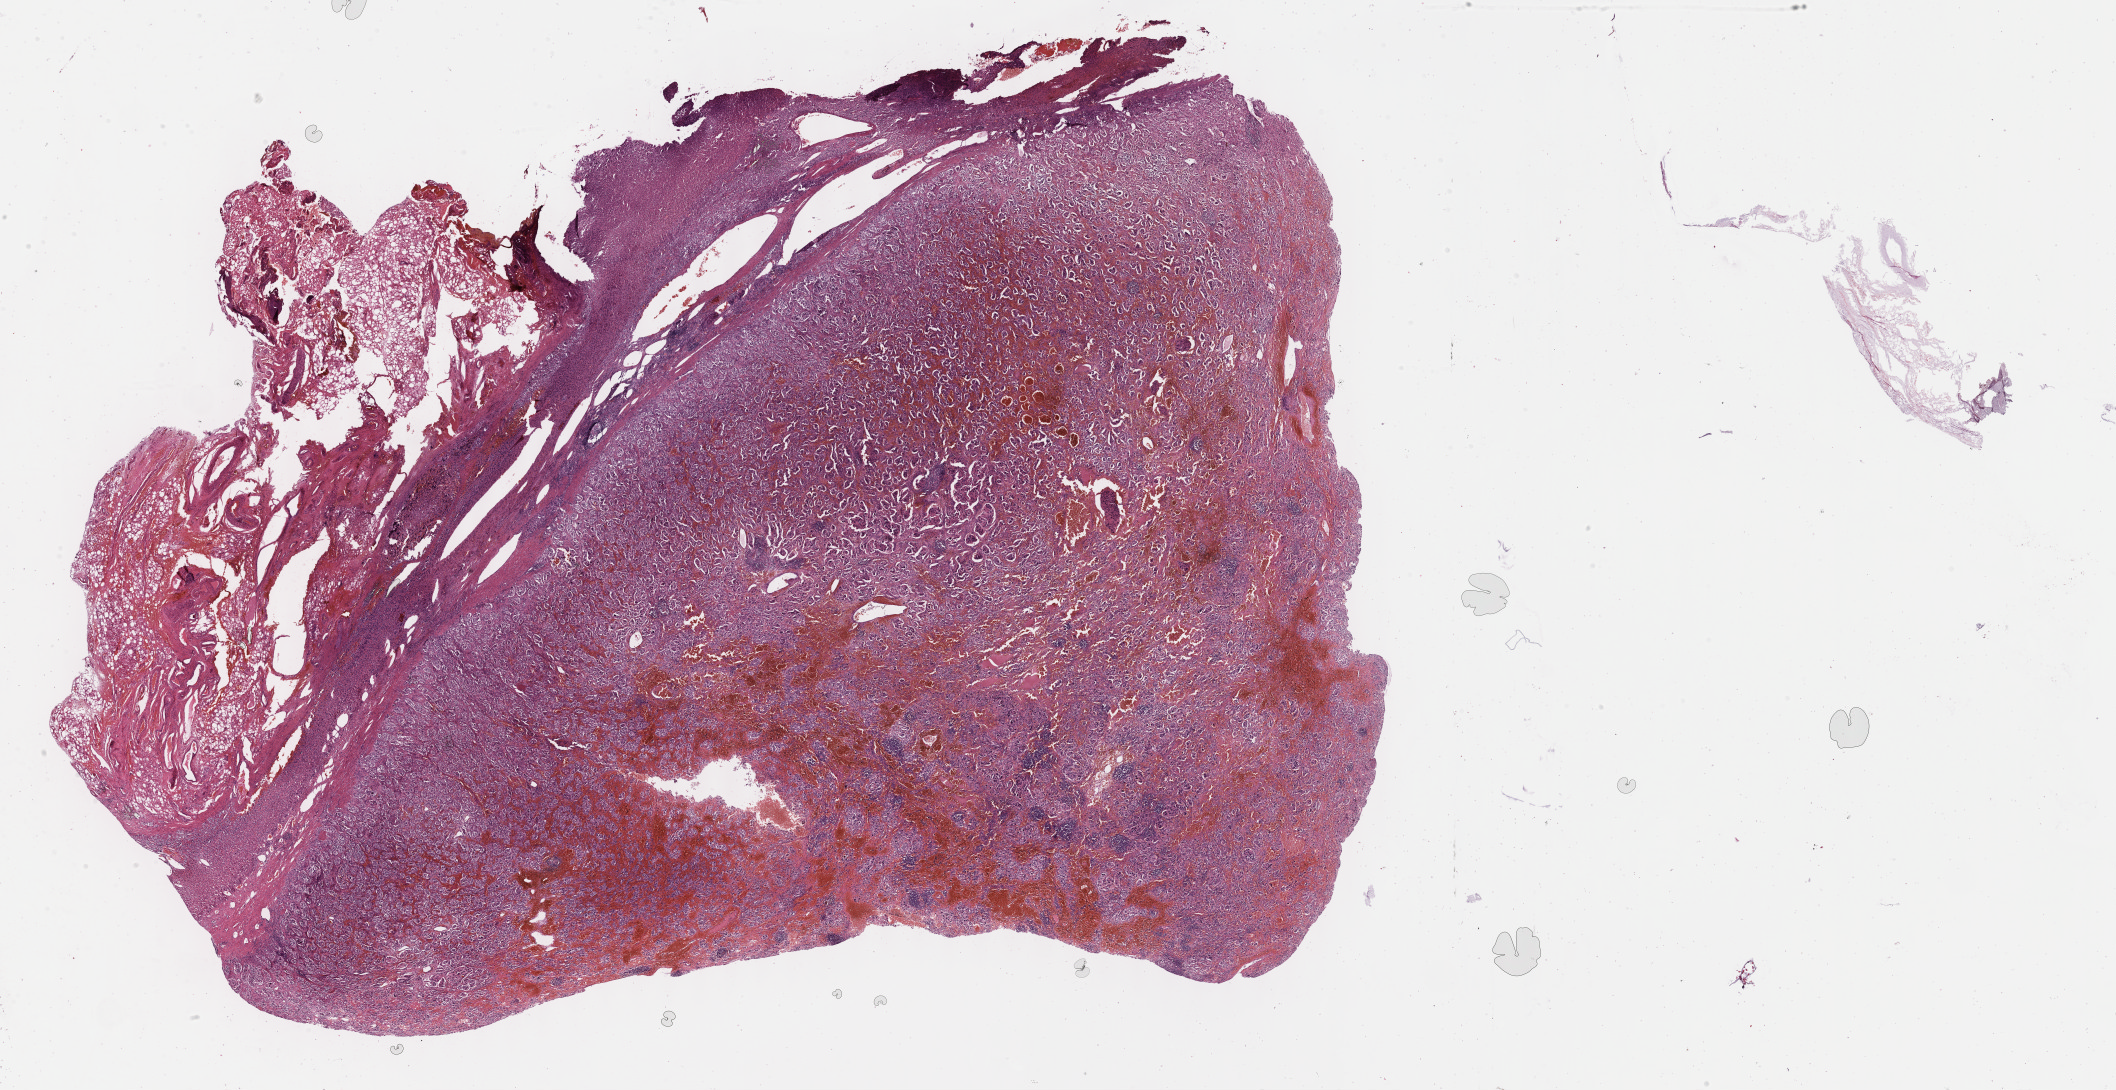
Hematoxylin and eosin (H&E) stained whole-slide image, low-resolution overview of the scanned area, about 34.2 x 17.6 mm (acquisition: 40x scan); formalin-fixed paraffin-embedded (FFPE) diagnostic section; adrenal gland, primary tumour sample. Male patient; age at initial diagnosis 19 years.
Laterality: right. Histologic diagnosis: Pheochromocytoma, malignant.